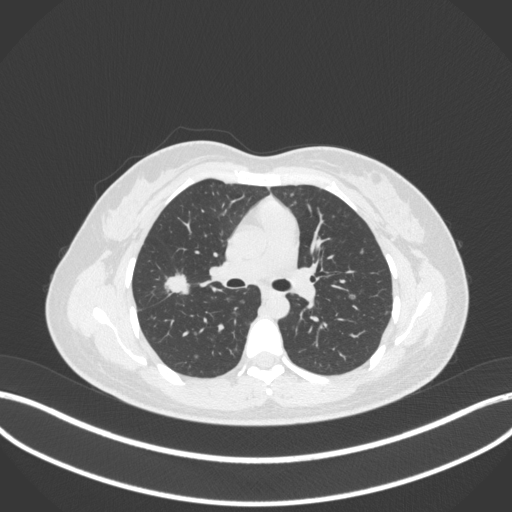
Chest CT, one axial slice; position 202 of 214 along the scan axis; reconstruction kernel B31f; lung window (W 1500 / L -600 HU); 1 mm slice thickness; 512 × 512 image matrix. Patient: female, 33 years. Case-level facts recorded for this patient, not image findings: clinical TNM (as recorded): T1c N0 M0; histopathological grade: G2-G3.
Annotated regions visible in this slice (rectangle marked by the reading radiologist):
- lung tumour (recorded histology: adenocarcinoma): bounding box [x1, y1, x2, y2] px = [160, 271, 198, 301]